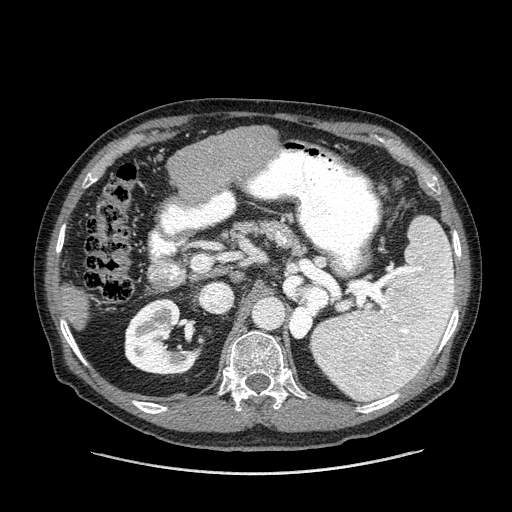
Contrast-enhanced abdominal CT (liver protocol), one axial slice; position 68 of 180 along the scan axis; reconstruction kernel STANDARD; 120 kVp; one of 2 acquisitions stored at this slice position; soft-tissue window (W 400 / L 40 HU); 2.5 mm slice thickness; 512 × 512 image matrix. From the clinical record (not read from this slice): diagnosis: hepatocellular carcinoma (patient treated with transarterial chemoembolisation; whether this scan precedes or follows treatment is not stated here); TNM stage (as recorded): Stage-II; Child-Pugh class: A.
Outlined on this slice (semi-automatic segmentation, software-assisted and operator-edited):
- liver parenchyma outside the tumour (the mass and vessels are separate outlines, so this box may not span the whole liver): bounding box [x1, y1, x2, y2] px = [60, 126, 276, 330]